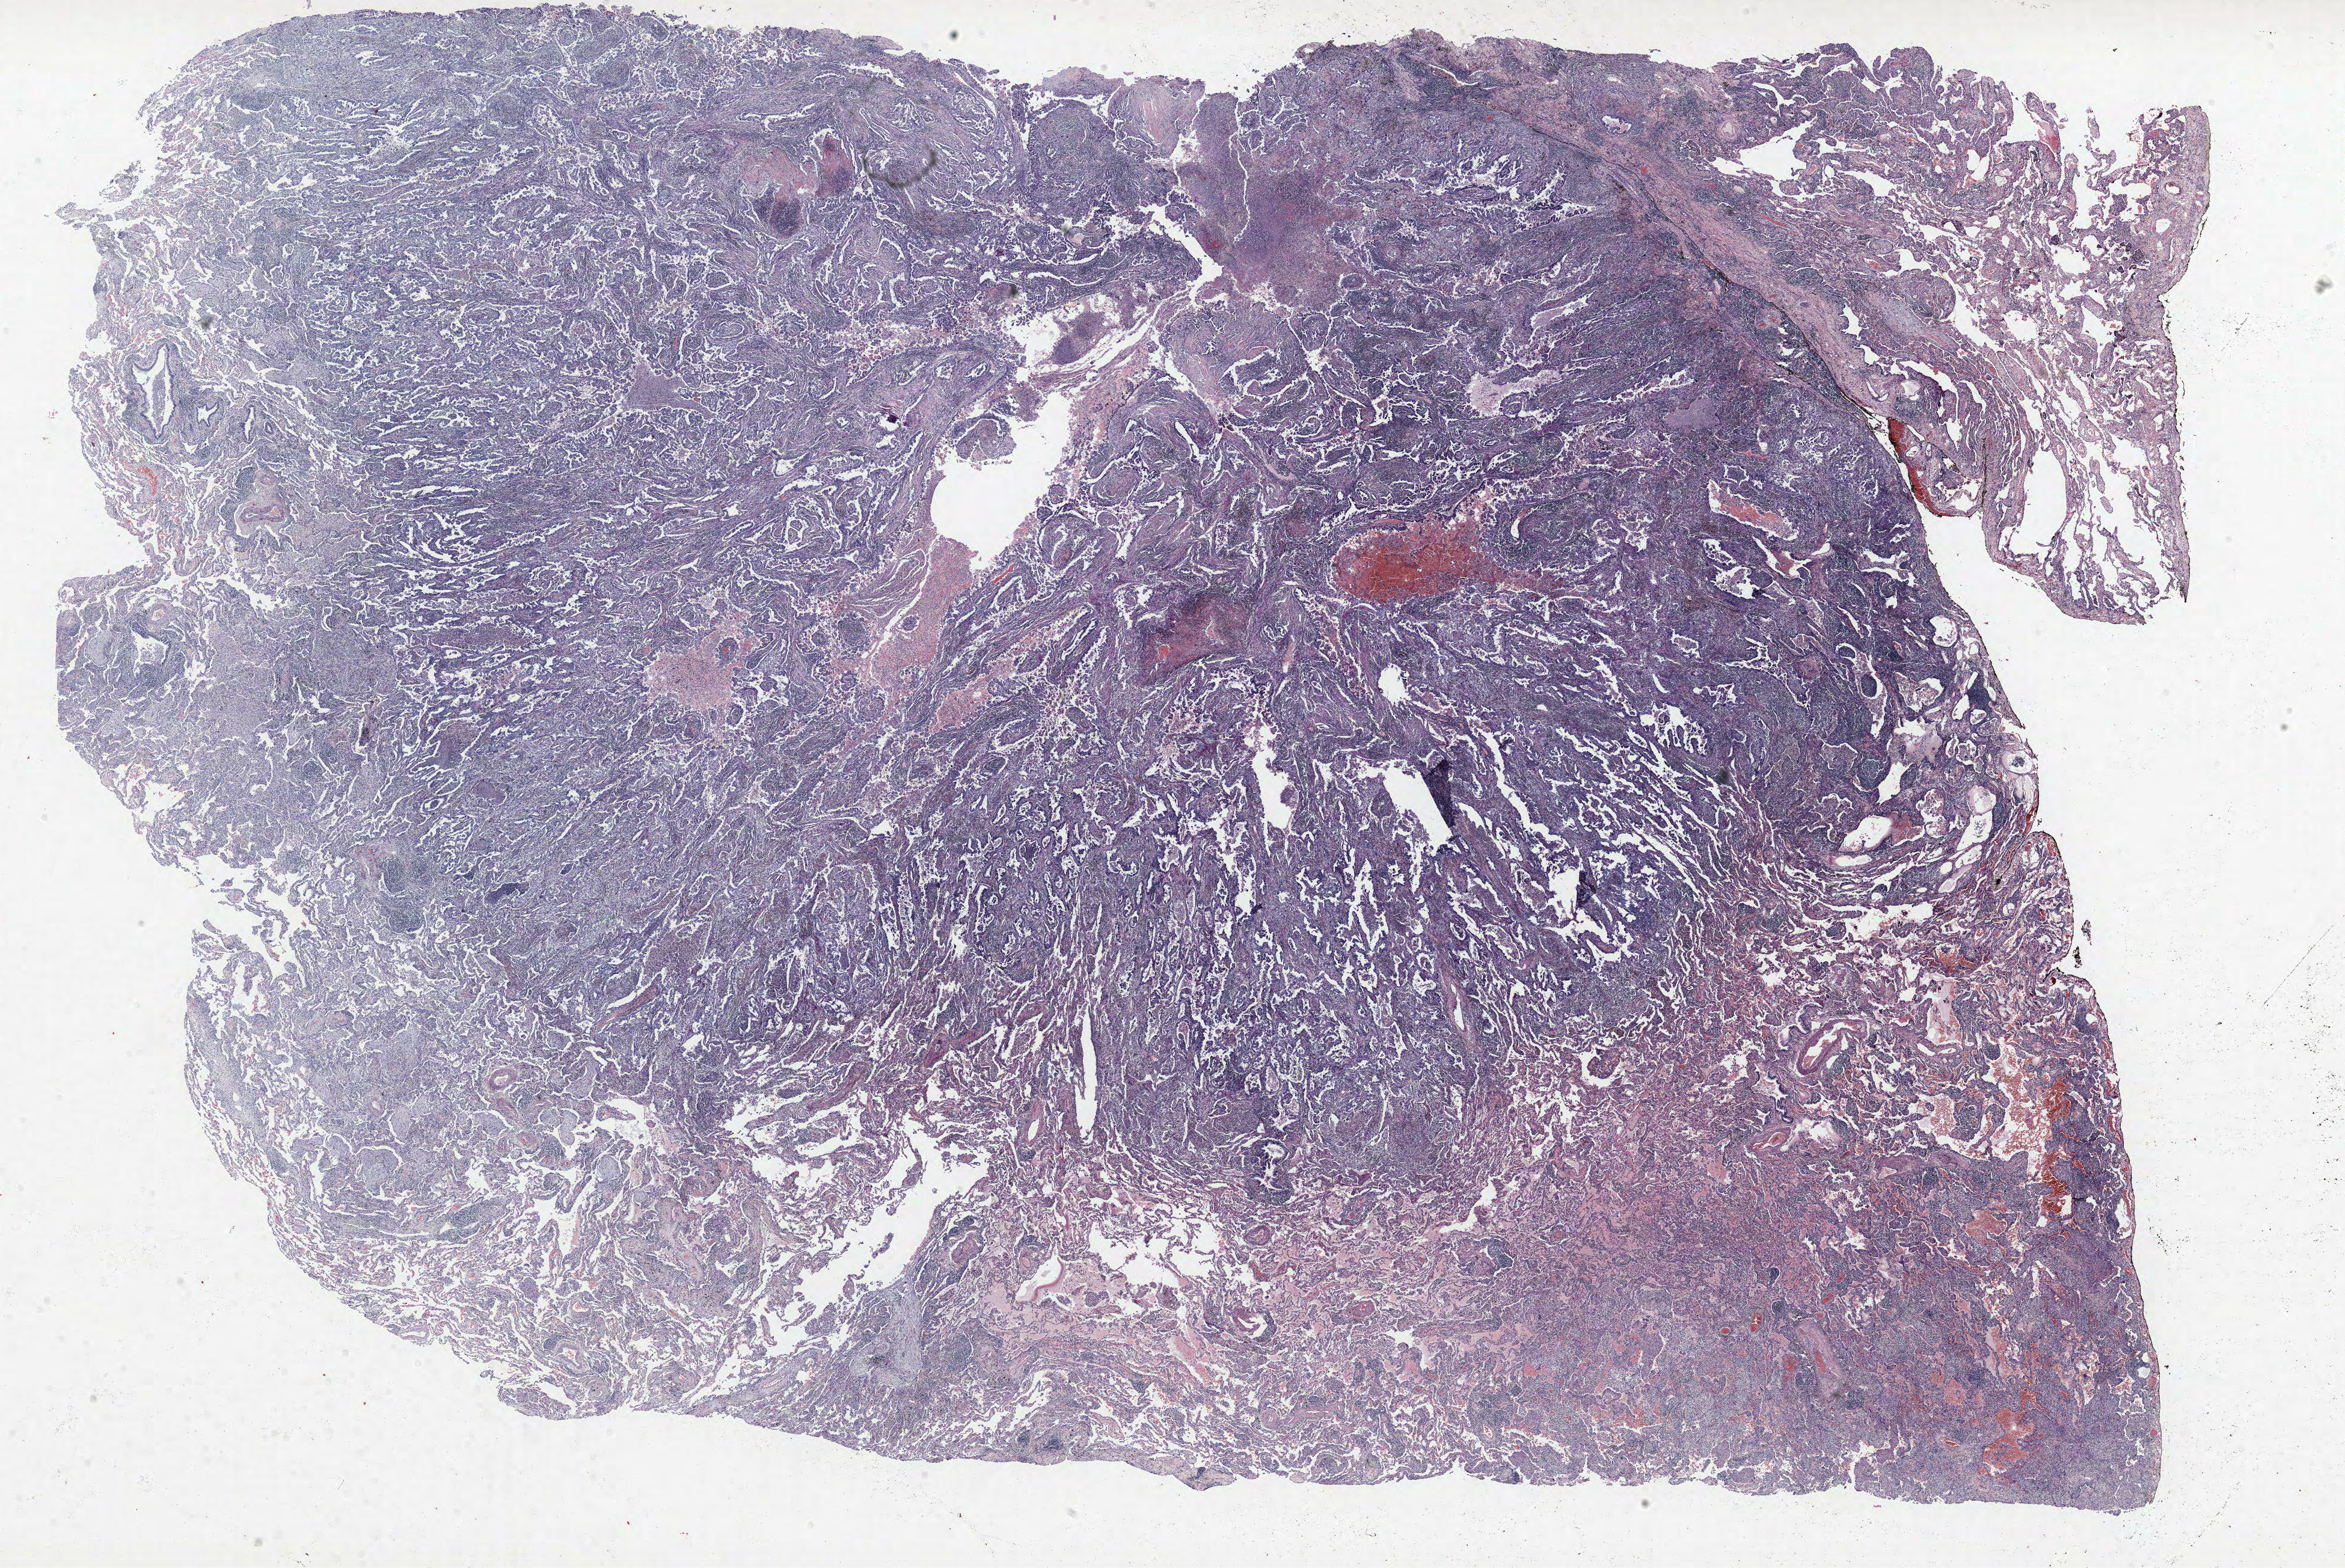
H&E whole-slide image — low-resolution overview of the scanned area, about 31.2 x 20.9 mm (acquisition: 40x scan); formalin-fixed paraffin-embedded (FFPE) section; lung tissue. Male, age 61 at enrolment. Former smoker at enrolment. Grade: well differentiated (G1).
ICD-O-3 topography: upper lobe of lung (C34.1). Tumour size (pathology): 45 mm. Stage (AJCC 6th edition): IIIA. Participant's lung-cancer diagnosis: Adenocarcinoma, NOS. Primary tumour location (clinical record): left upper lobe.